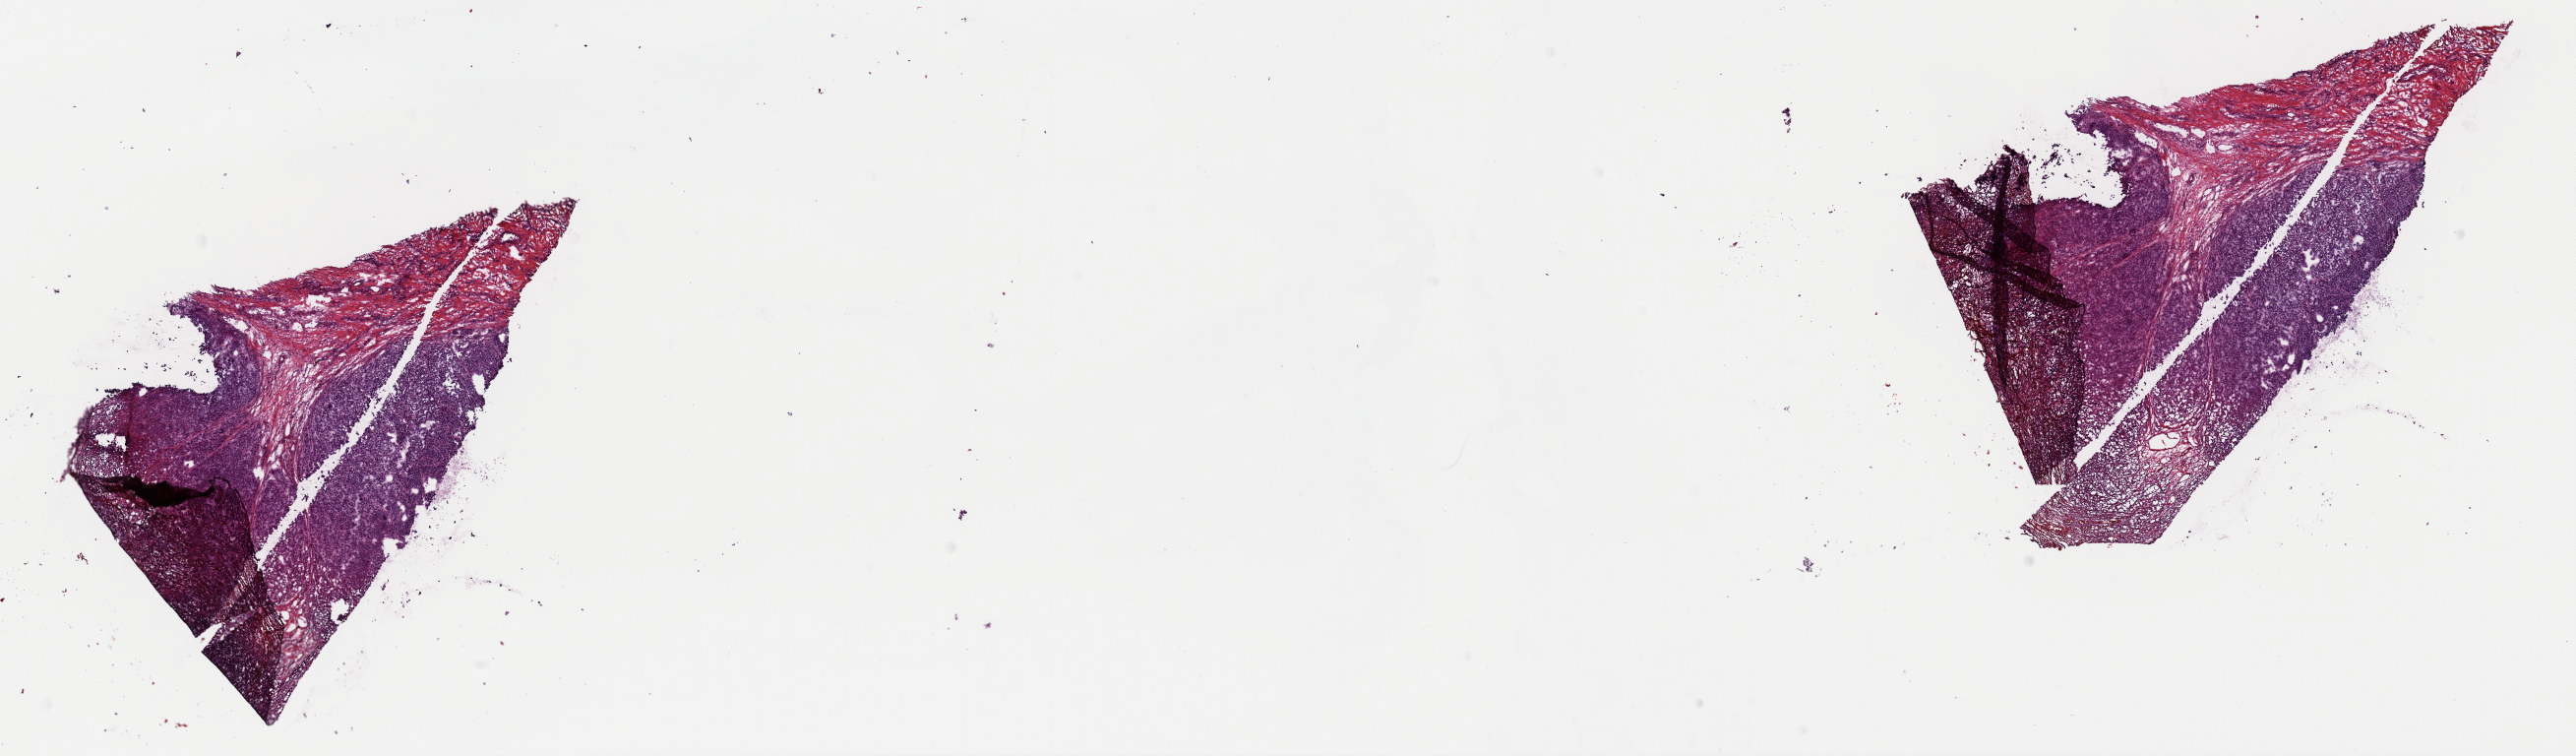
H&E-stained whole-slide image — a low-resolution overview of the entire scanned area, about 20.7 x 6.1 mm (from a 40x scan); frozen section from the top of the tissue portion; skin, primary tumour sample. Male patient; age at initial diagnosis 74 years.
Pathologic diagnosis: Malignant melanoma, NOS.